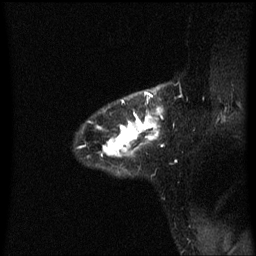
Breast MRI (dynamic contrast-enhanced), one sagittal slice; slice 46 of 60 in the series (ordered by position); dynamic contrast-enhanced series, image 2 of 3 at this slice position (ordered by acquisition); 1.5 T; TE 4.2 ms, TR 8.4 ms; 2 mm slice thickness; 256 × 256 image matrix, field of view 200 × 200 mm. Patient: female, 32 years.
Annotated regions visible in this slice (semi-automatically segmented with operator editing):
- analysis volume of interest (the breast-tissue region the enhancement analysis was run in; not a lesion): bounding box <81,86,164,165> (left, top, right, bottom; pixels)
- tumour enhancement mask (voxels above the 70 % enhancement threshold inside the analysis volume of interest): <97,92,163,157>